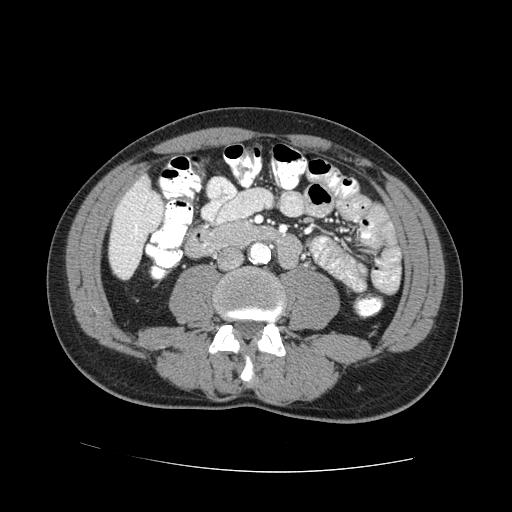
Contrast-enhanced abdominal CT (liver protocol), one axial slice. Slice 9 of 73 in the series (ordered by position). Reconstruction kernel STANDARD. One of 2 acquisitions stored at this slice position. Soft-tissue window (W 400 / L 40 HU). 2.5 mm slice thickness. 512 × 512 image matrix, field of view 380 × 380 mm. Case-level facts recorded for this patient, not image findings: diagnosis: hepatocellular carcinoma (patient treated with transarterial chemoembolisation; whether this scan precedes or follows treatment is not stated here); TNM stage (as recorded): Stage-IVA; Child-Pugh class: A; tumour differentiation: no biopsy; tumour nodularity: uninodular.
Annotated regions visible in this slice (semi-automatic segmentation, software-assisted and operator-edited):
- liver parenchyma outside the tumour (the mass and vessels are separate outlines, so this box may not span the whole liver): bounding box (x1, y1, x2, y2) in pixels: (108, 174, 164, 278)
- liver vessels: (135, 207, 154, 234)